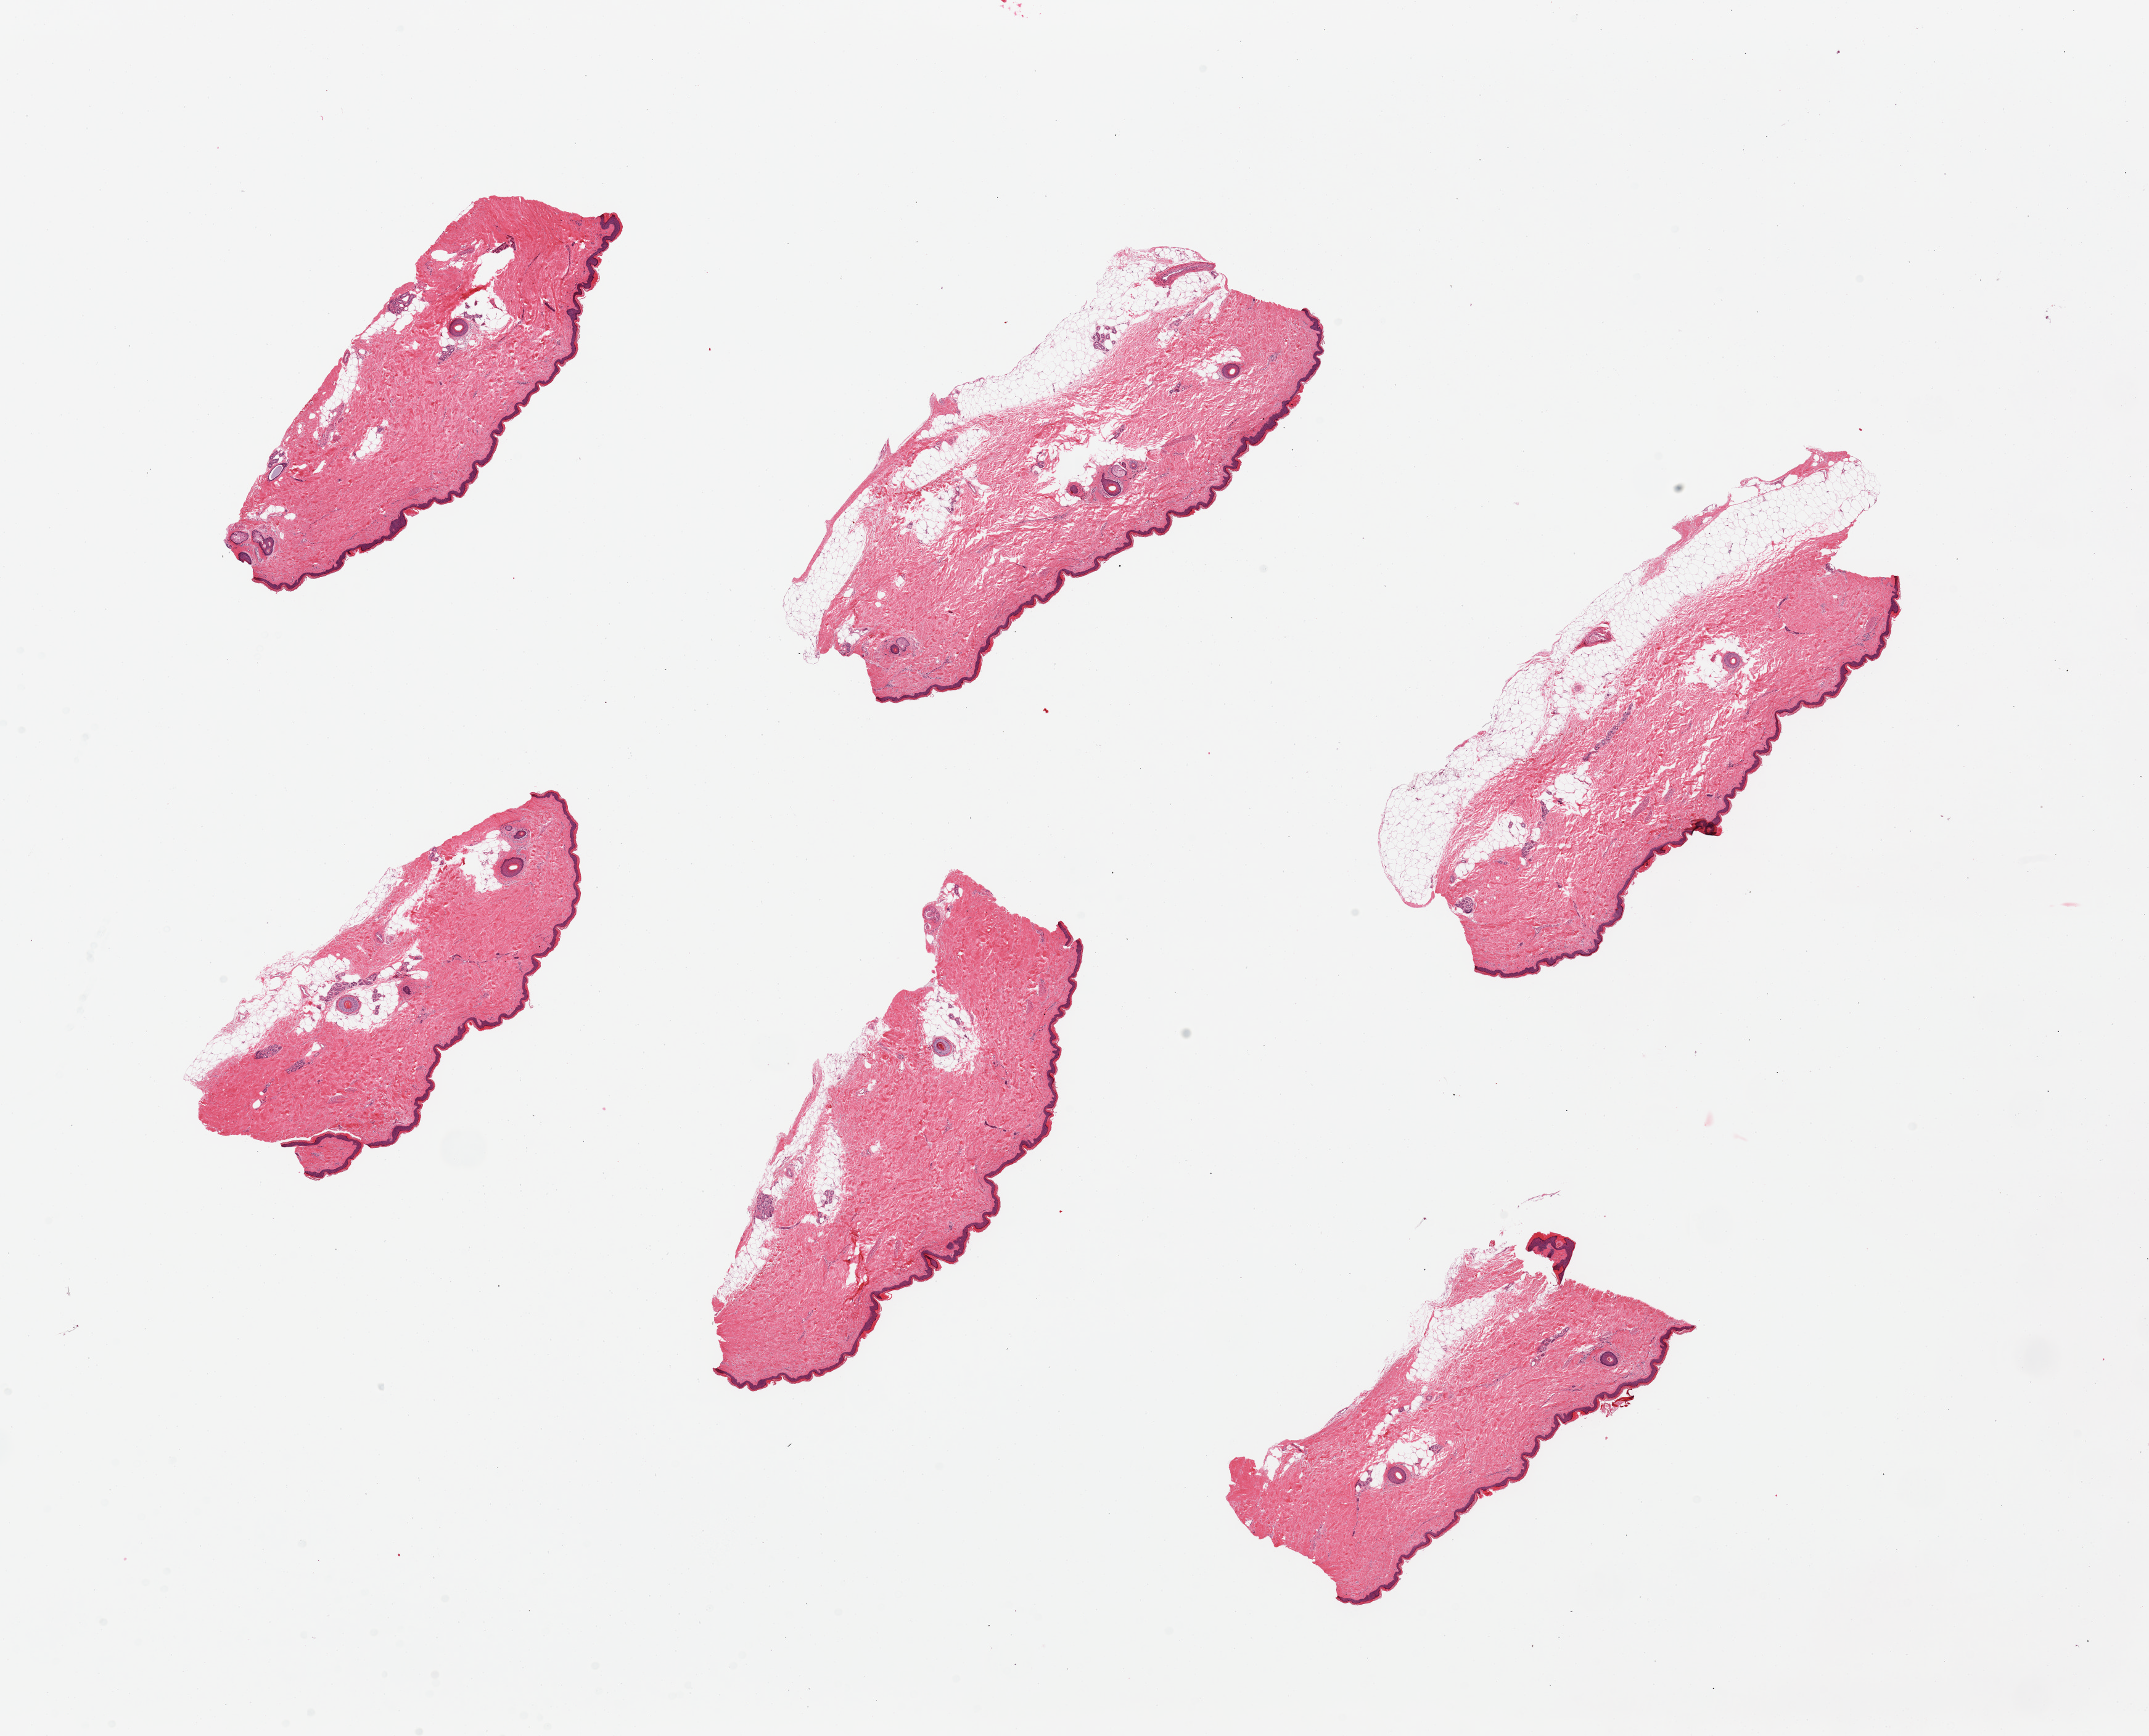
Digitized haematoxylin and eosin-stained section — a low-resolution overview of the entire scanned area, about 27.6 x 22.3 mm, PAXgene-fixed, paraffin-embedded tissue, target tissue: skin of lower leg, donor tissue sample. Donor sex: male.
Review note (as recorded): 6 pieces. Up to 1 mm subcutaneous fat.